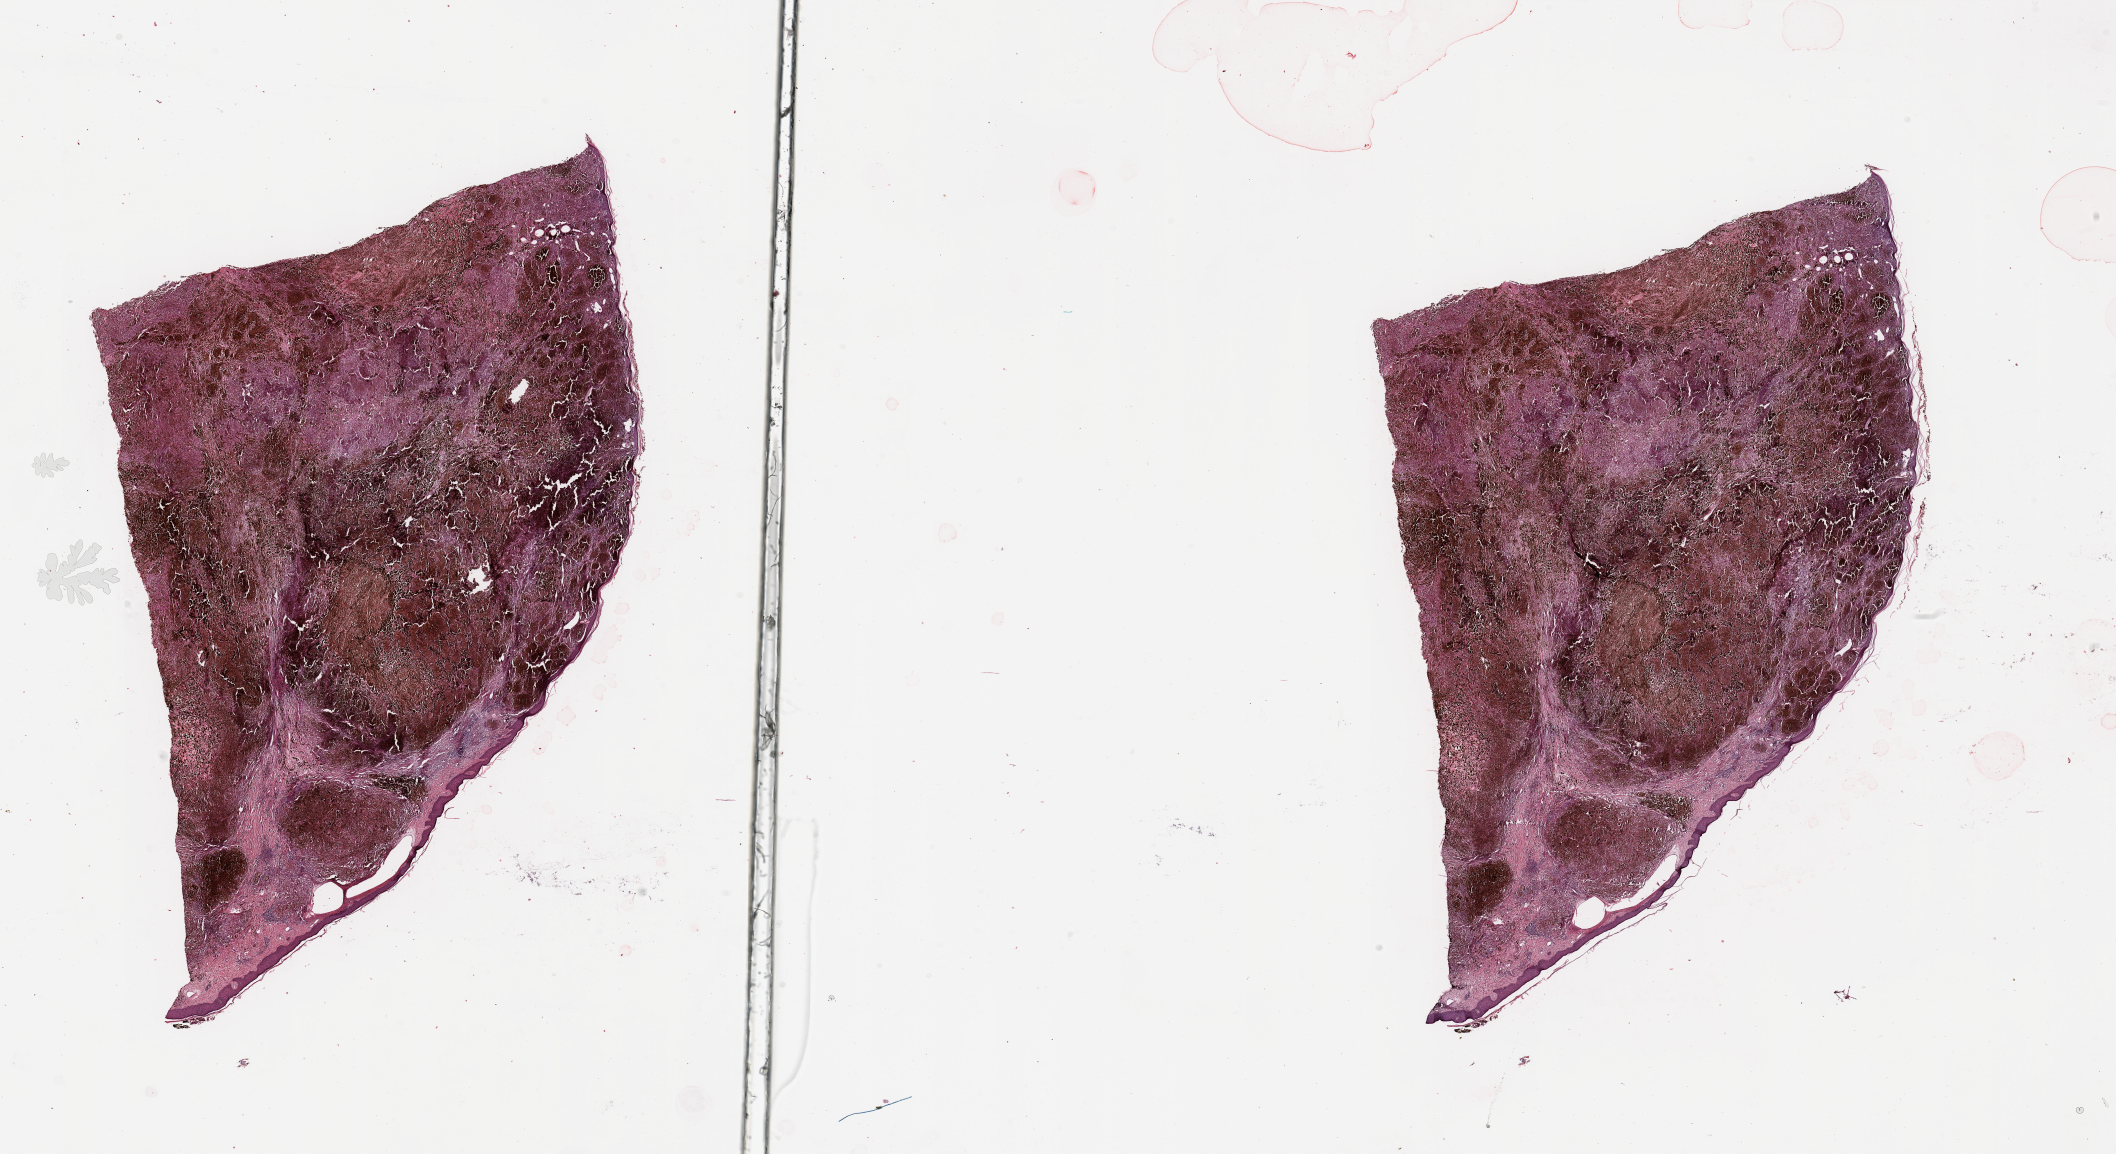
H&E-stained whole-slide image — a low-resolution overview of the entire scanned area, about 33.5 x 18.3 mm (acquisition: 20x scan), melanoma tumour tissue; sampled site not recorded. Patient: male, age 66 years.
• AJCC pathologic stage: IV
• histologic diagnosis: Malignant melanoma, NOS
• primary tumour site (as recorded): trunk